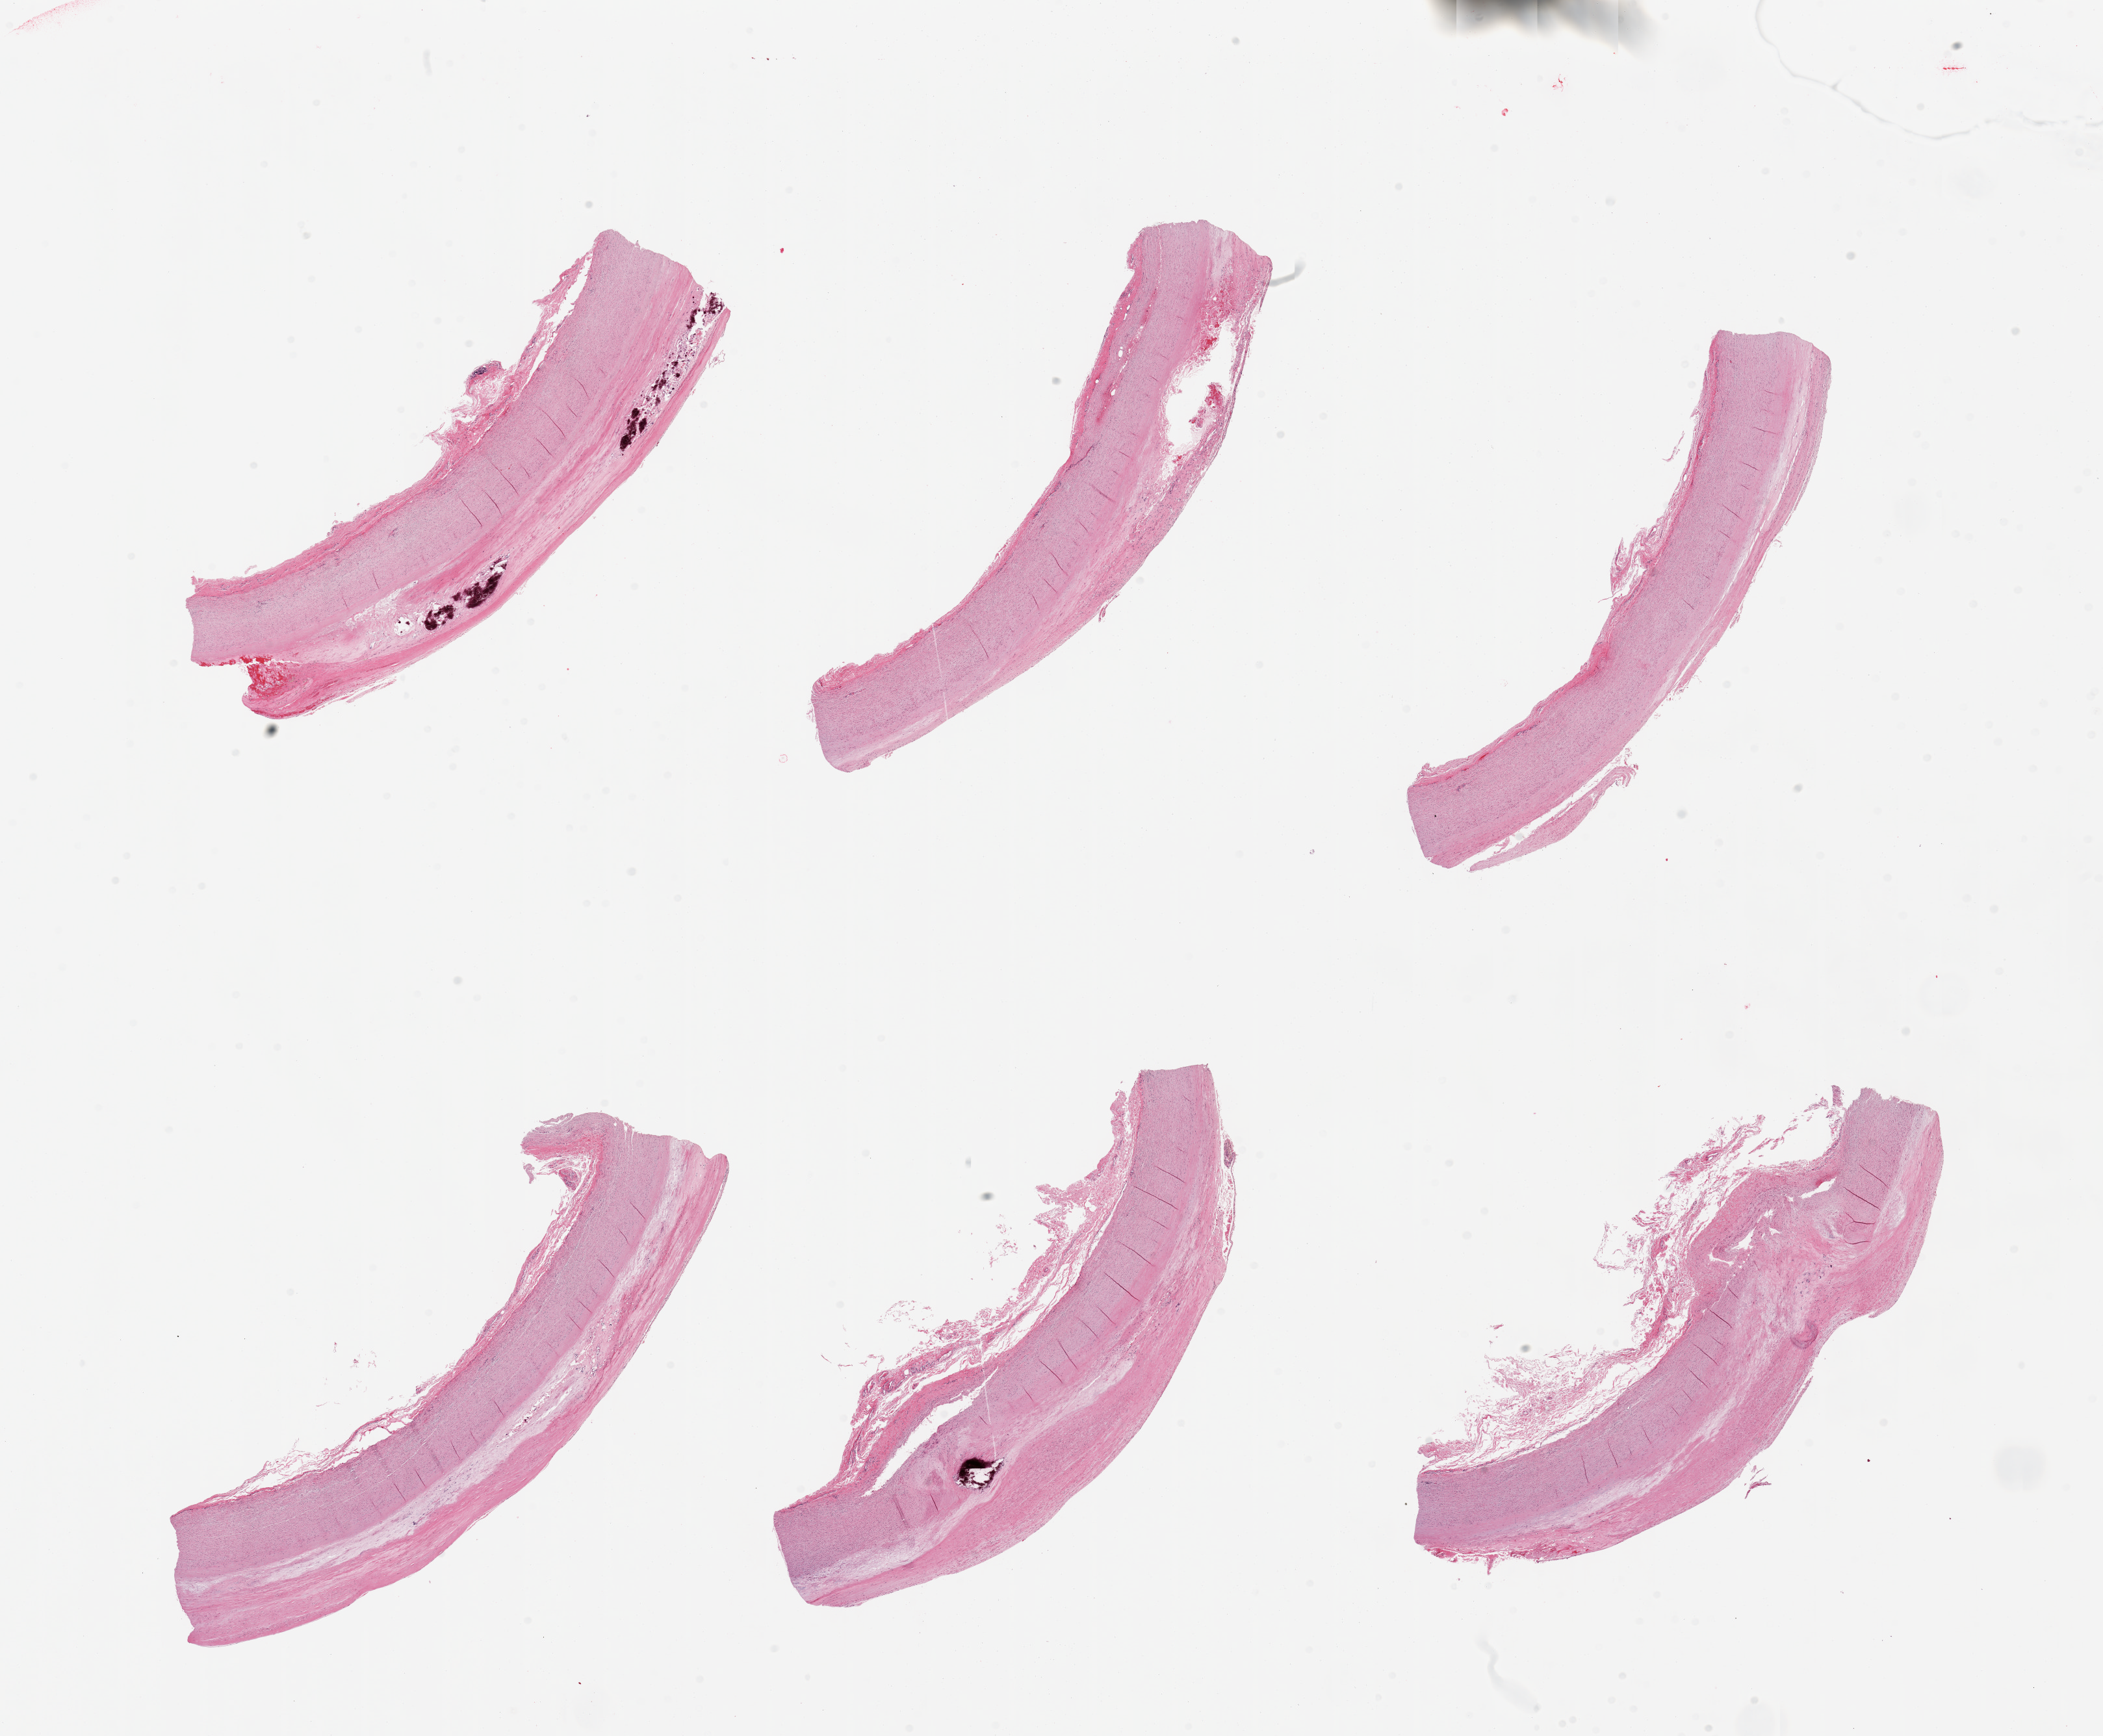
H&E whole-slide image, low-resolution overview of the scanned area, about 25.6 x 21.1 mm (from a 20x scan); PAXgene-fixed, paraffin-embedded tissue; section of aorta (target tissue); donor tissue sample. Donor sex: female.
- review note (as recorded): 6 pieces, ~1mm calcifying atherosis layer